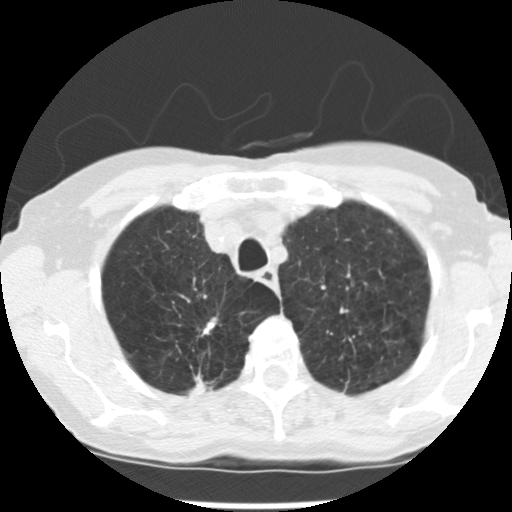
Low-dose screening chest CT, axial slice; baseline screening round; lung window (W 1500 / L -600 HU); standard (soft-tissue) reconstruction kernel (STANDARD); slice 42 of 265 in the series. Female, age 72 years at enrolment. Current smoker at enrolment.
2 expert-annotated lung lesions on this slice (largest first), box from (x=182, y=369) to (x=228, y=406) px; (x=186, y=310)–(x=231, y=346). The screening reader recorded 3 non-calcified nodules or masses ≥4 mm on this exam; which of them these boxes mark is not recorded. Participant outcome: lung cancer diagnosed 50 days after this screen — adenocarcinoma, NOS, right upper lobe, moderately differentiated (G2), stage IB (AJCC 6th edition), 22 mm at pathology.